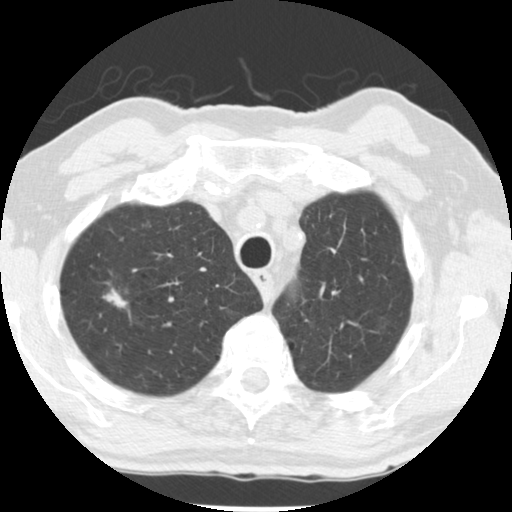
Low-dose screening chest CT, one axial slice; position 208 of 252 along the scan axis; lung window (W 1500 / L -600 HU); 2.5 mm slice thickness; 512 × 512 image matrix.
Annotated regions visible in this slice (manually delineated by an expert):
- lesion 1 (tumor, upper lobe of right lung): bounding box [x1, y1, x2, y2] px = [102, 288, 130, 312]